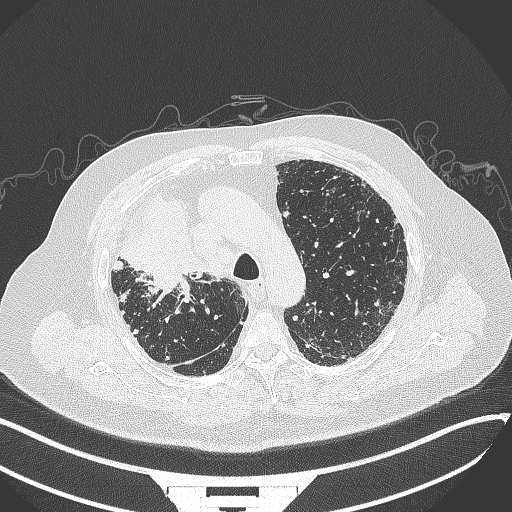
Chest CT, one axial slice; slice 260 of 384 in the series (ordered by position); reconstruction kernel B70f; 120 kVp; lung window (W 1500 / L -600 HU); 1 mm slice thickness; 512 × 512 image matrix. Male patient, age 69 years. Case-level facts recorded for this patient, not image findings: clinical TNM (as recorded): T4 N3 M1.
Outlined on this slice (bounding box drawn by a radiologist):
- lung tumour (recorded histology: adenocarcinoma): box from (x=119, y=200) to (x=205, y=299) px